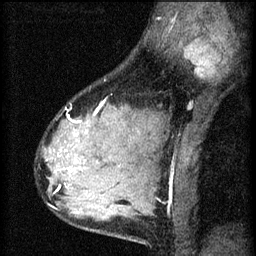
Breast MRI (dynamic contrast-enhanced), one sagittal slice. 3 images stored at this slice position (order not interpretable as contrast timing). 1.5 T. TE 4.2 ms, TR 8.2 ms. 256 × 256 image matrix, field of view 180 × 180 mm. Female patient, age 37 years.
Structures marked on this image (semi-automatic segmentation, software-assisted and operator-edited):
- analysis volume of interest (the breast-tissue region the enhancement analysis was run in; not a lesion): bounding box (x1, y1, x2, y2) in pixels: (44, 106, 119, 197)
- tumour enhancement mask (voxels above the 70 % enhancement threshold inside the analysis volume of interest): (61, 122, 88, 187)